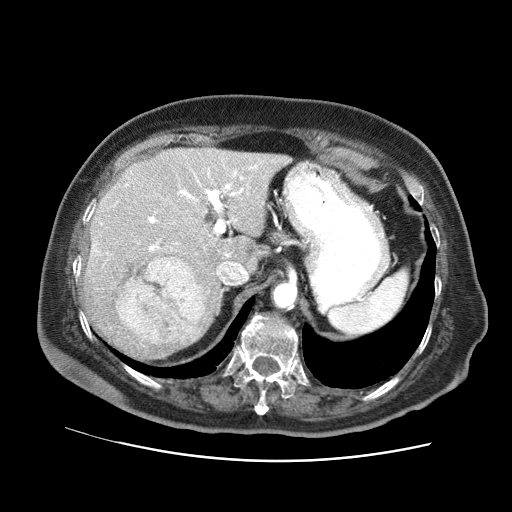
Contrast-enhanced abdominal CT (liver protocol), one axial slice. Position 46 of 73 along the scan axis. Reconstruction kernel STANDARD. 120 kVp. Soft-tissue window (W 400 / L 40 HU). 512 × 512 image matrix, field of view 380 × 380 mm. Case-level facts recorded for this patient, not image findings: diagnosis: hepatocellular carcinoma (patient treated with transarterial chemoembolisation; whether this scan precedes or follows treatment is not stated here); TNM stage (as recorded): Stage-I; Child-Pugh class: A; tumour nodularity: uninodular.
Annotated regions visible in this slice (semi-automatically segmented with operator editing):
- liver parenchyma outside the tumour (the mass and vessels are separate outlines, so this box may not span the whole liver): bounding box (x1, y1, x2, y2) in pixels: (80, 148, 290, 363)
- mass: (118, 258, 204, 342)
- liver vessels: (94, 164, 258, 257)